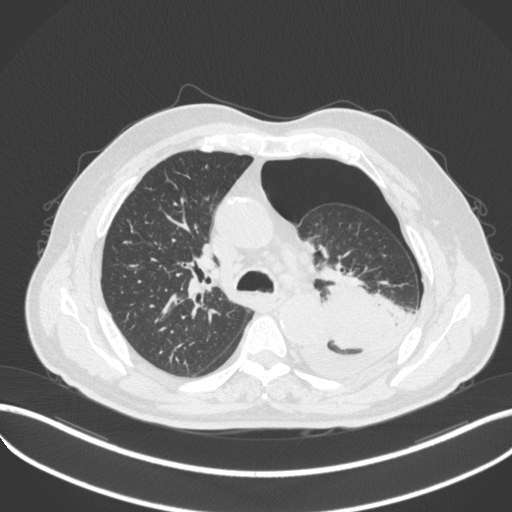
Chest CT, one axial slice. Slice 342 of 466 in the series (ordered by position). Reconstruction kernel B31f. 120 kVp. Lung window (W 1500 / L -600 HU). 1 mm slice thickness. 512 × 512 image matrix, field of view 400 × 400 mm. Patient: male, 76 years. From the clinical record (not read from this slice): clinical TNM (as recorded): T3 N0 M1b.
Outlined on this slice (bounding box drawn by a radiologist):
- lung tumour (recorded histology: adenocarcinoma): bounding box [x1, y1, x2, y2] px = [298, 281, 408, 386]